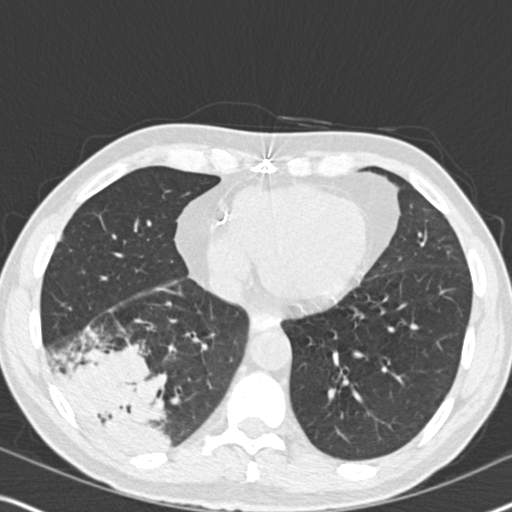
Low-dose screening chest CT, one axial slice; slice 69 of 182 in the series (ordered by position); reconstruction kernel B30f; 120 kVp; lung window (W 1500 / L -600 HU); 512 × 512 image matrix, field of view 330 × 330 mm.
Structures marked on this image (outlined manually by an expert reader):
- lesion 1 (tumor, lower lobe of right lung): bounding box [x1, y1, x2, y2] px = [60, 348, 171, 454]